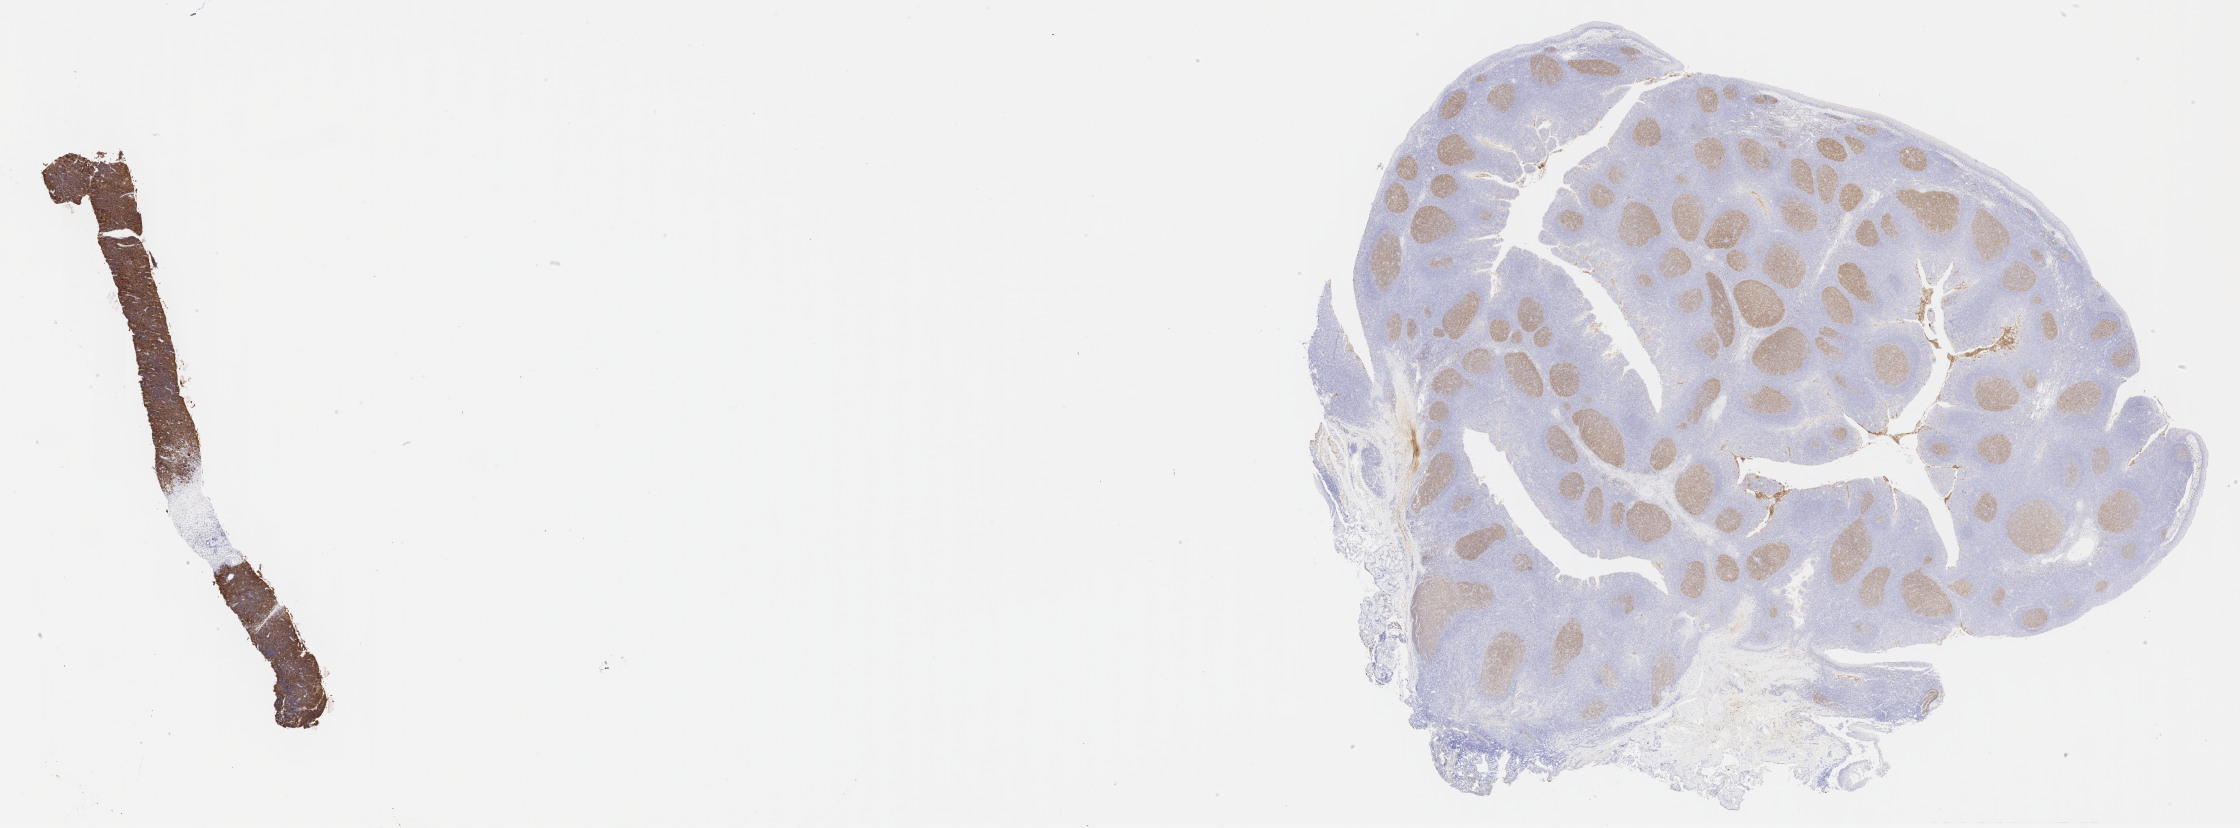
Immunohistochemistry (IHC) whole-slide image stained for CD10 — low-resolution overview of the scanned area, about 36.2 x 13.4 mm; specimen: tumor tissue. Male patient; age at initial diagnosis 7 years.
- histologic diagnosis: Neoplasm, uncertain whether benign or malignant